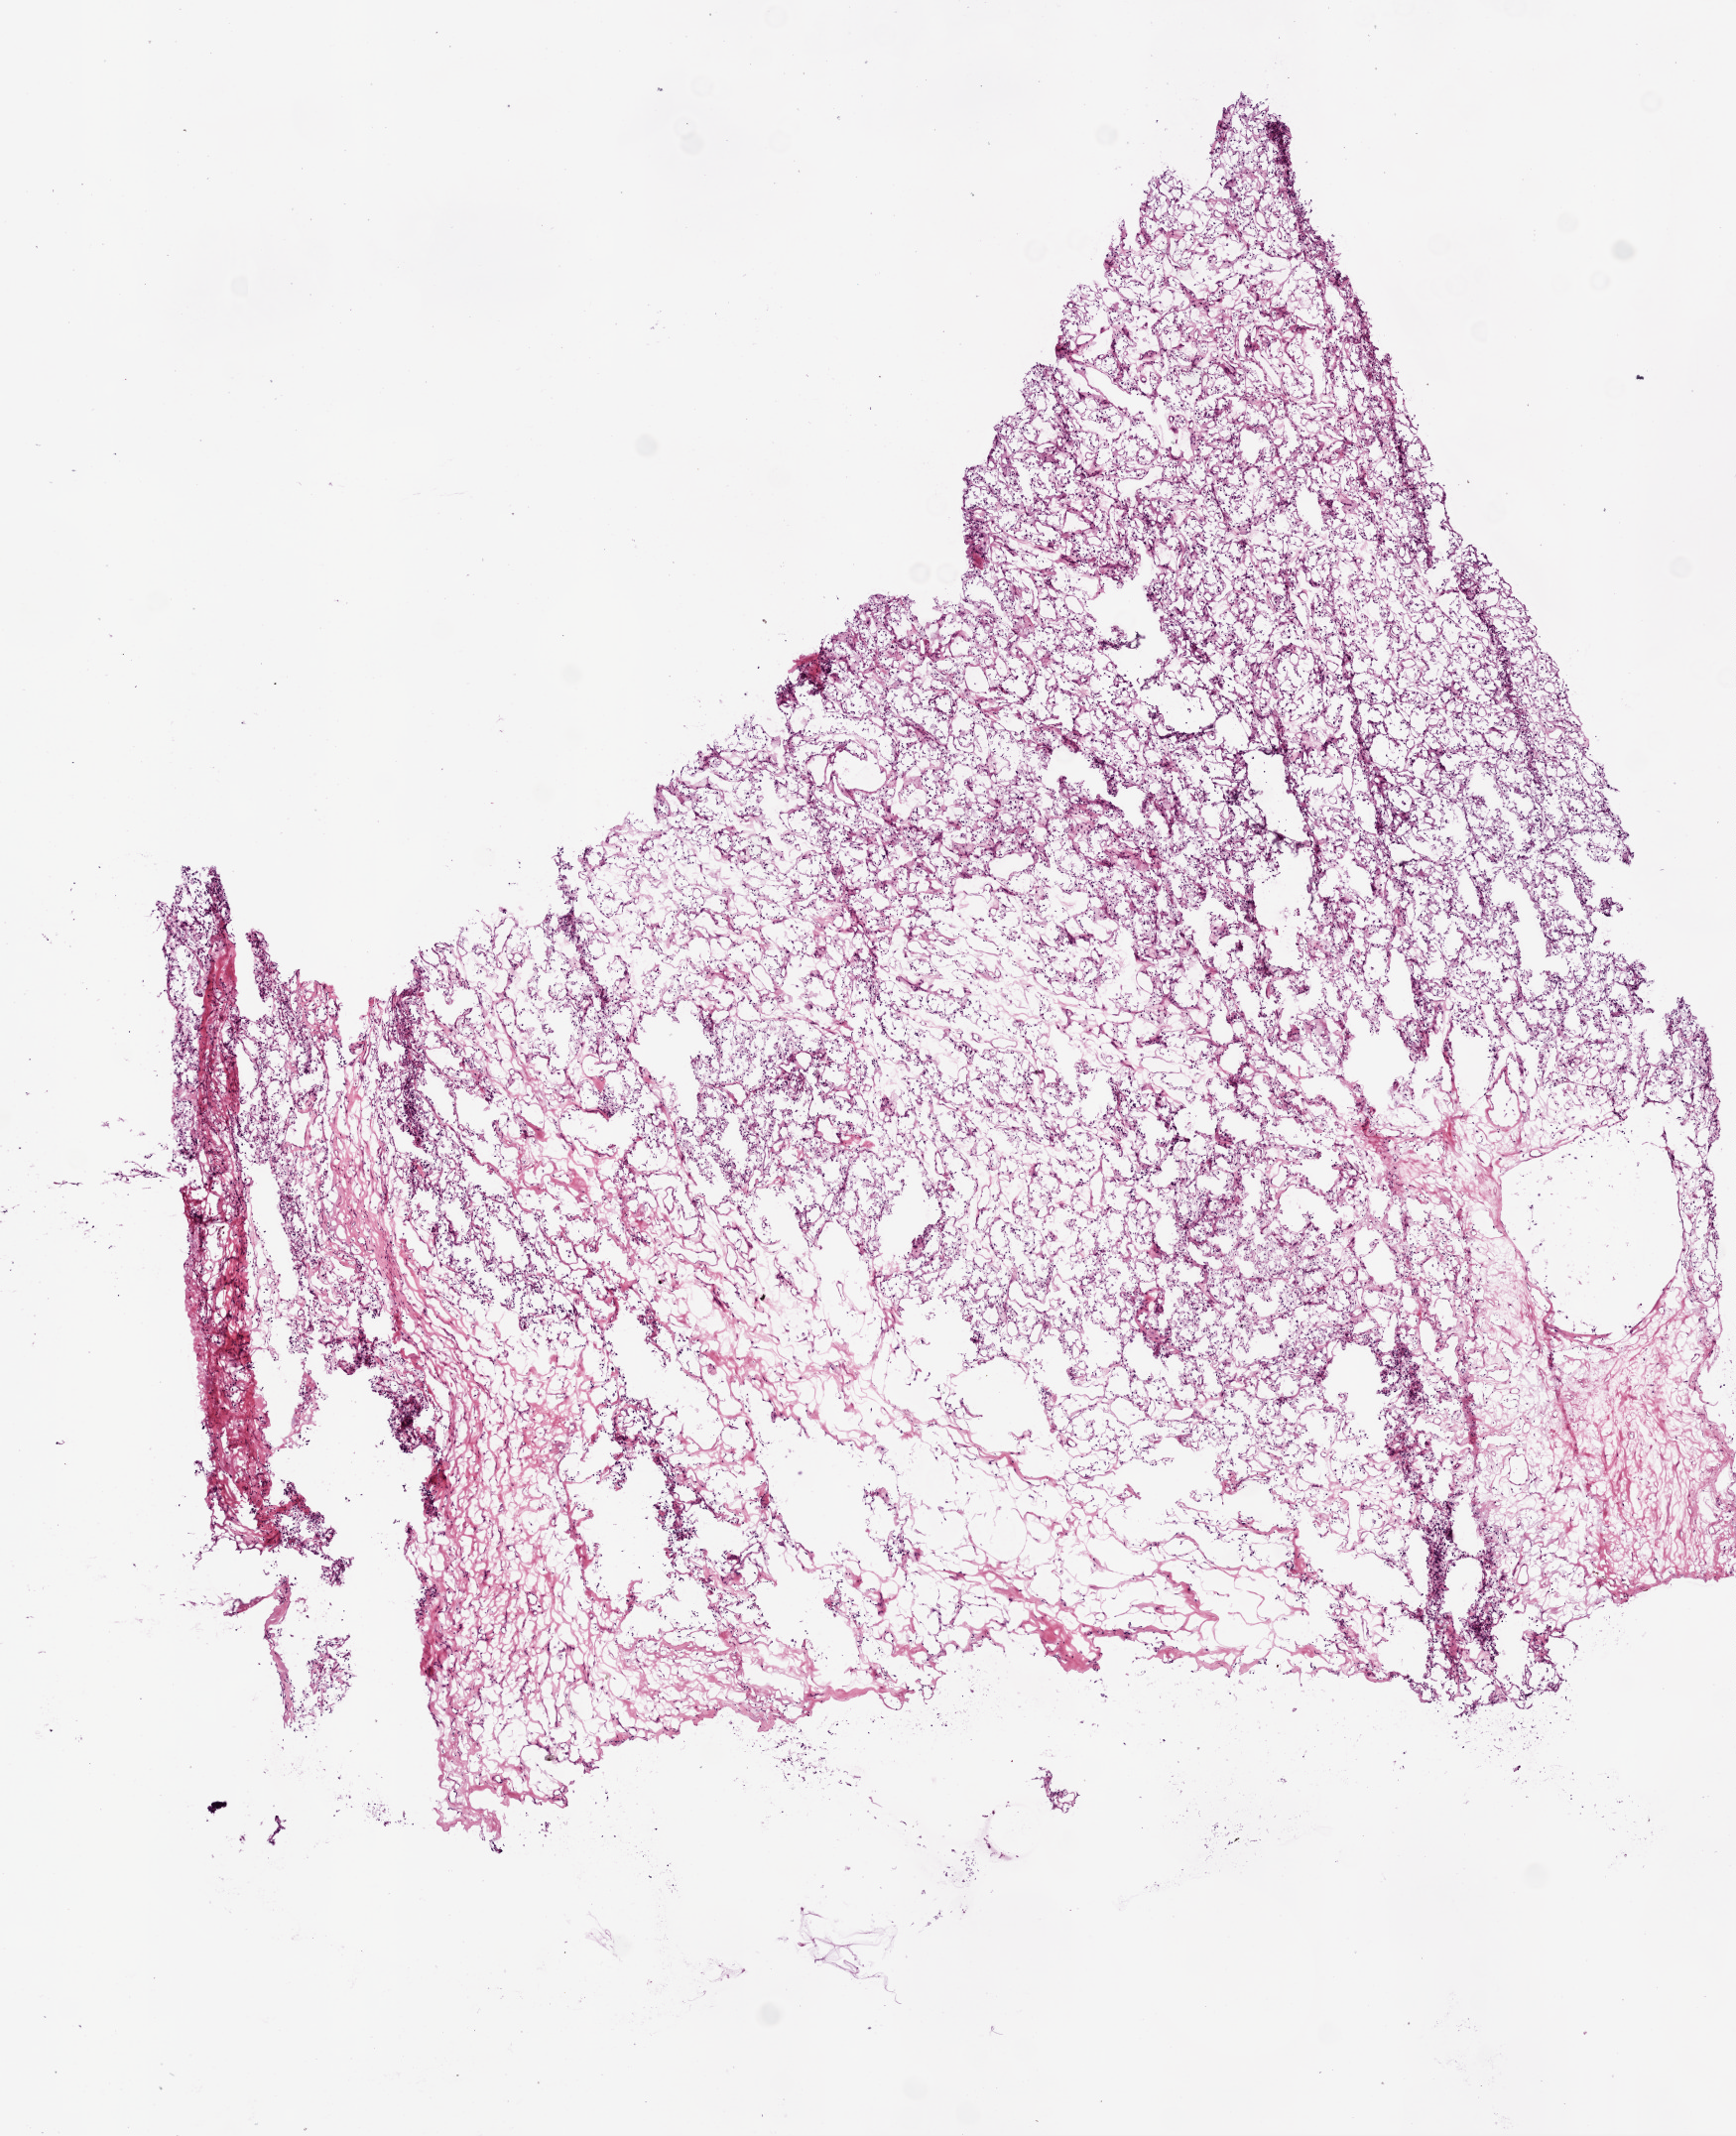
H&E-stained whole-slide image — whole scanned area (about 7.0 x 8.6 mm) shown as a low-resolution overview; frozen section; sample: primary tumour, kidney. Patient: male, age at initial diagnosis 63 years. Histologic grade: G3 (poorly differentiated). Pathologist review of this section (percent, as recorded): tumour cells 90%, tumour nuclei 85%, normal cells 0%, stromal cells 10%, necrosis 0%.
TNM: T2 NX M1. Histologic diagnosis: Clear cell adenocarcinoma, NOS. AJCC pathologic stage: IV. Laterality: left.